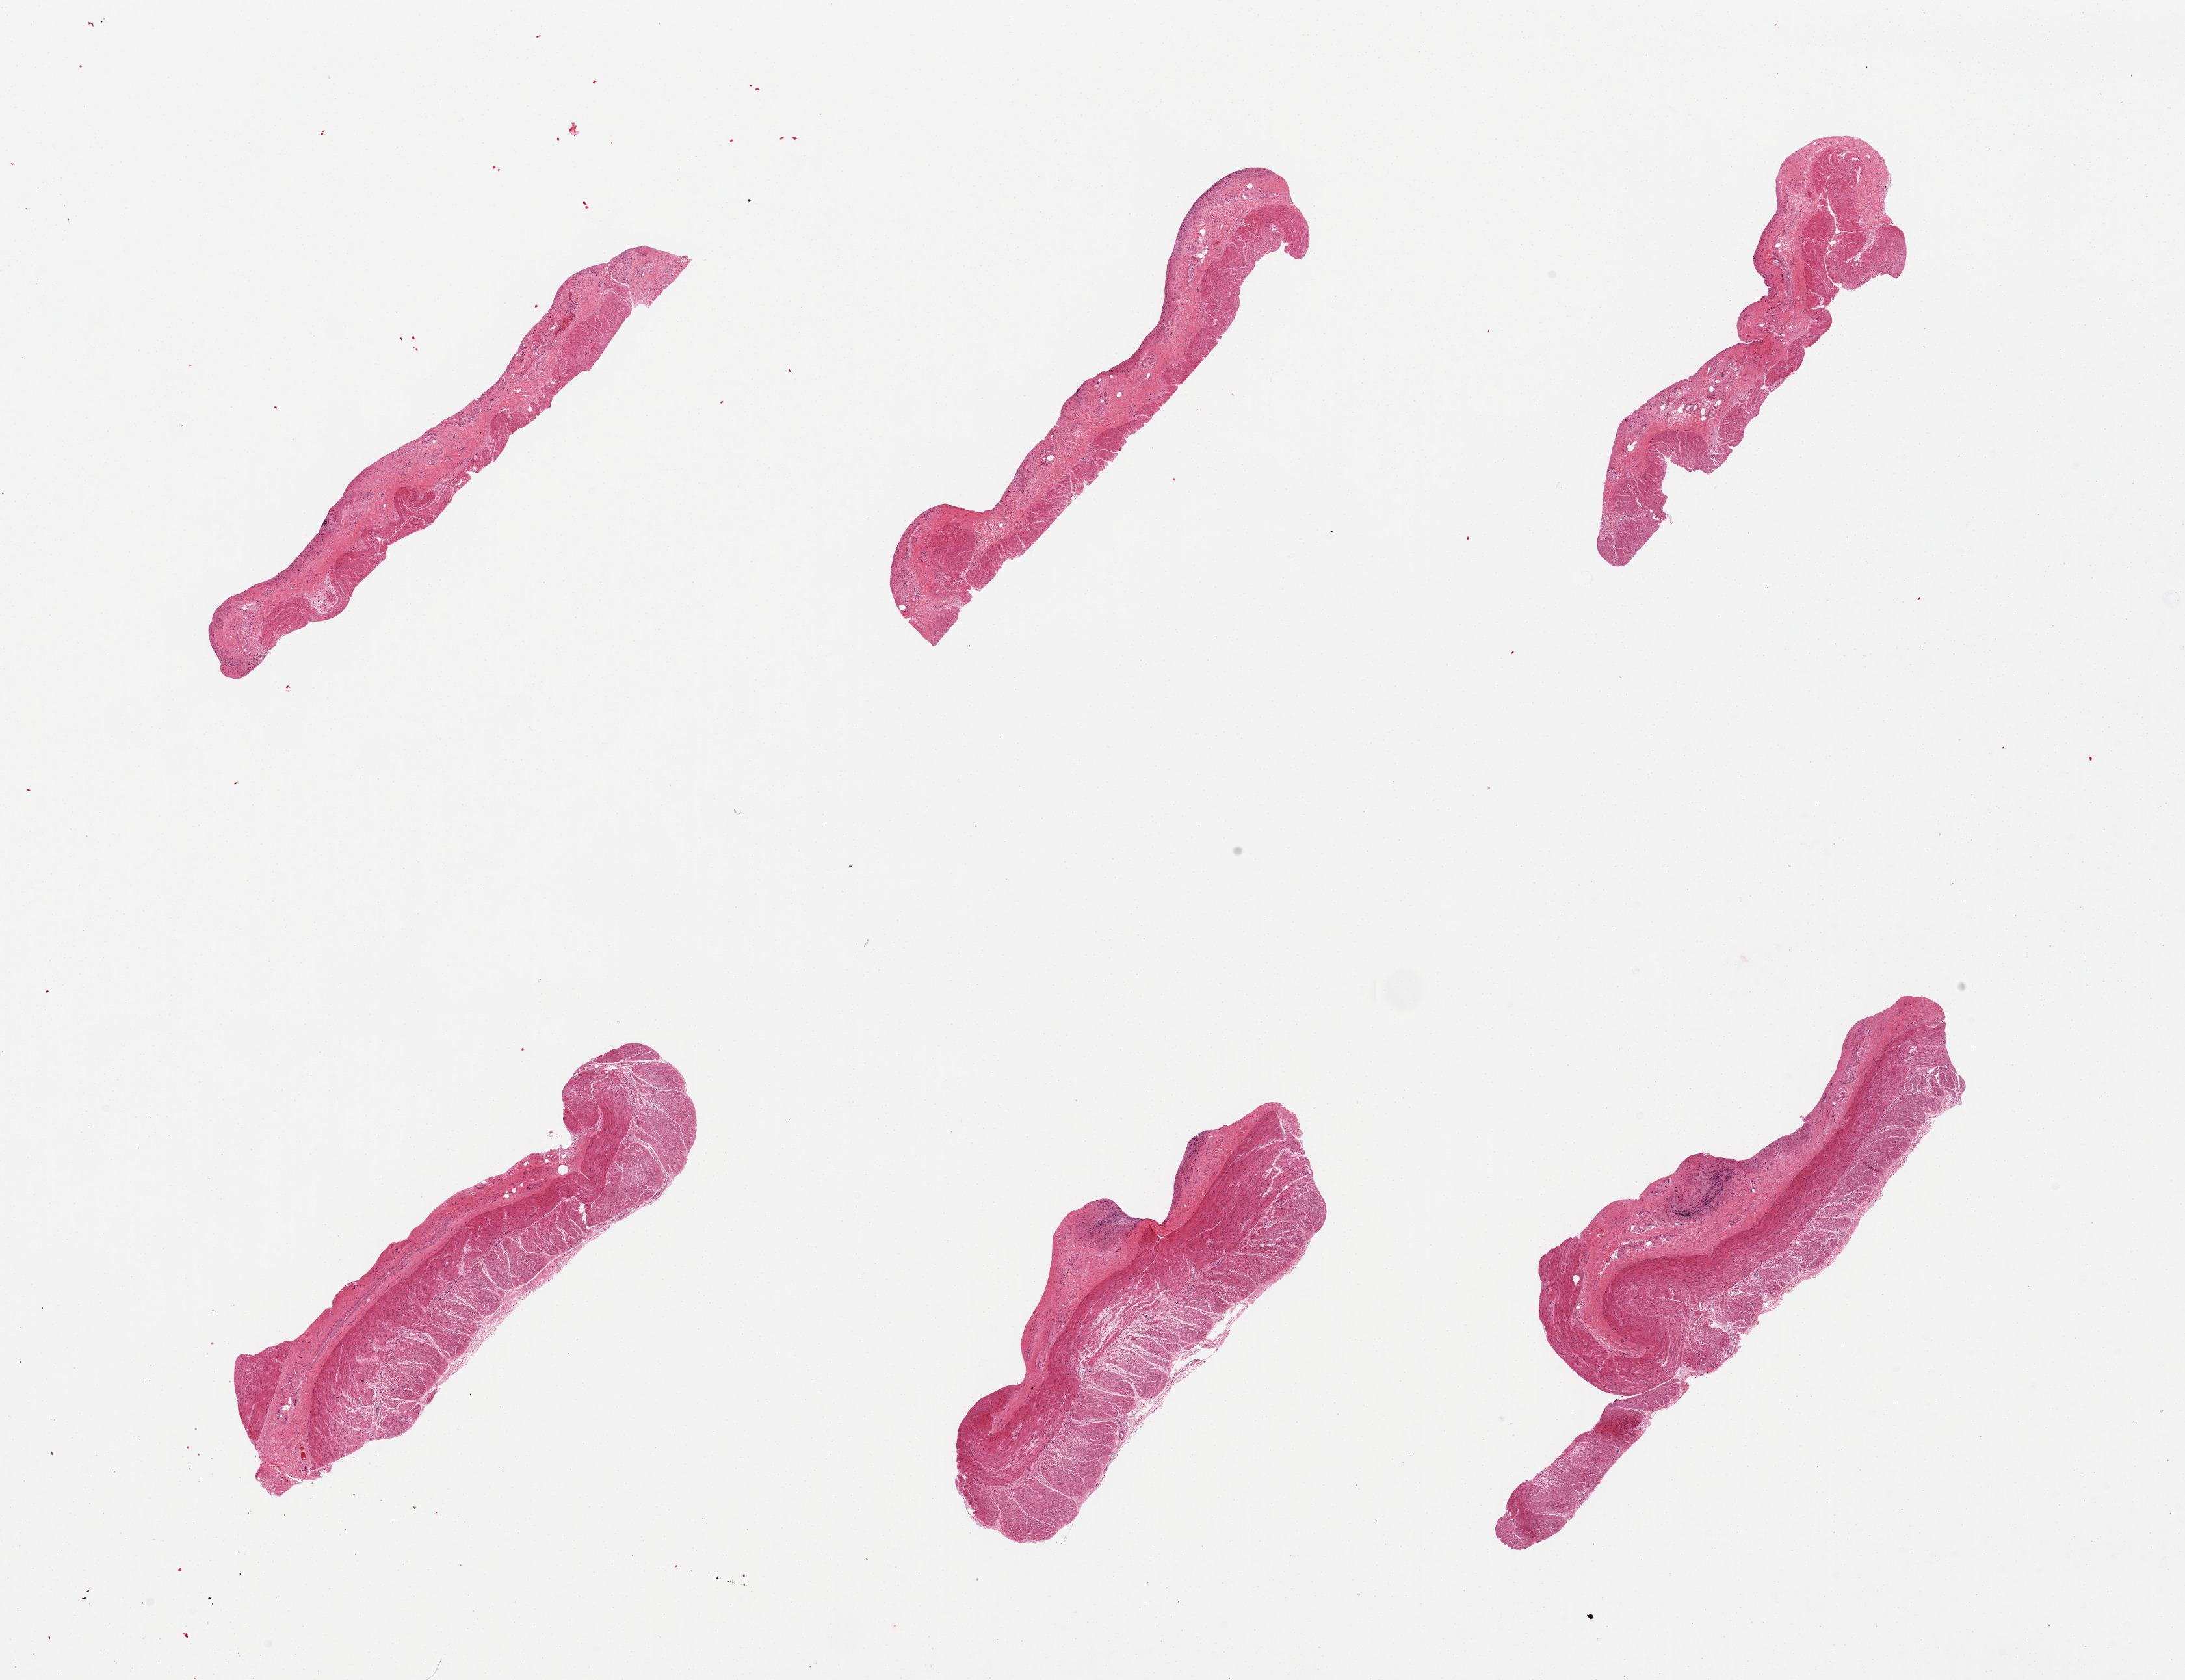
Whole-slide image, hematoxylin and eosin (H&E) stain, brightfield — whole scanned area (about 26.6 x 20.4 mm, acquisition: 20x scan) shown as a low-resolution overview; PAXgene-fixed, paraffin-embedded tissue; target tissue: sigmoid colon; tissue donor sample. Female donor.
* review note (as recorded): 6 pieces; varying amounts of muscularis and submucosa